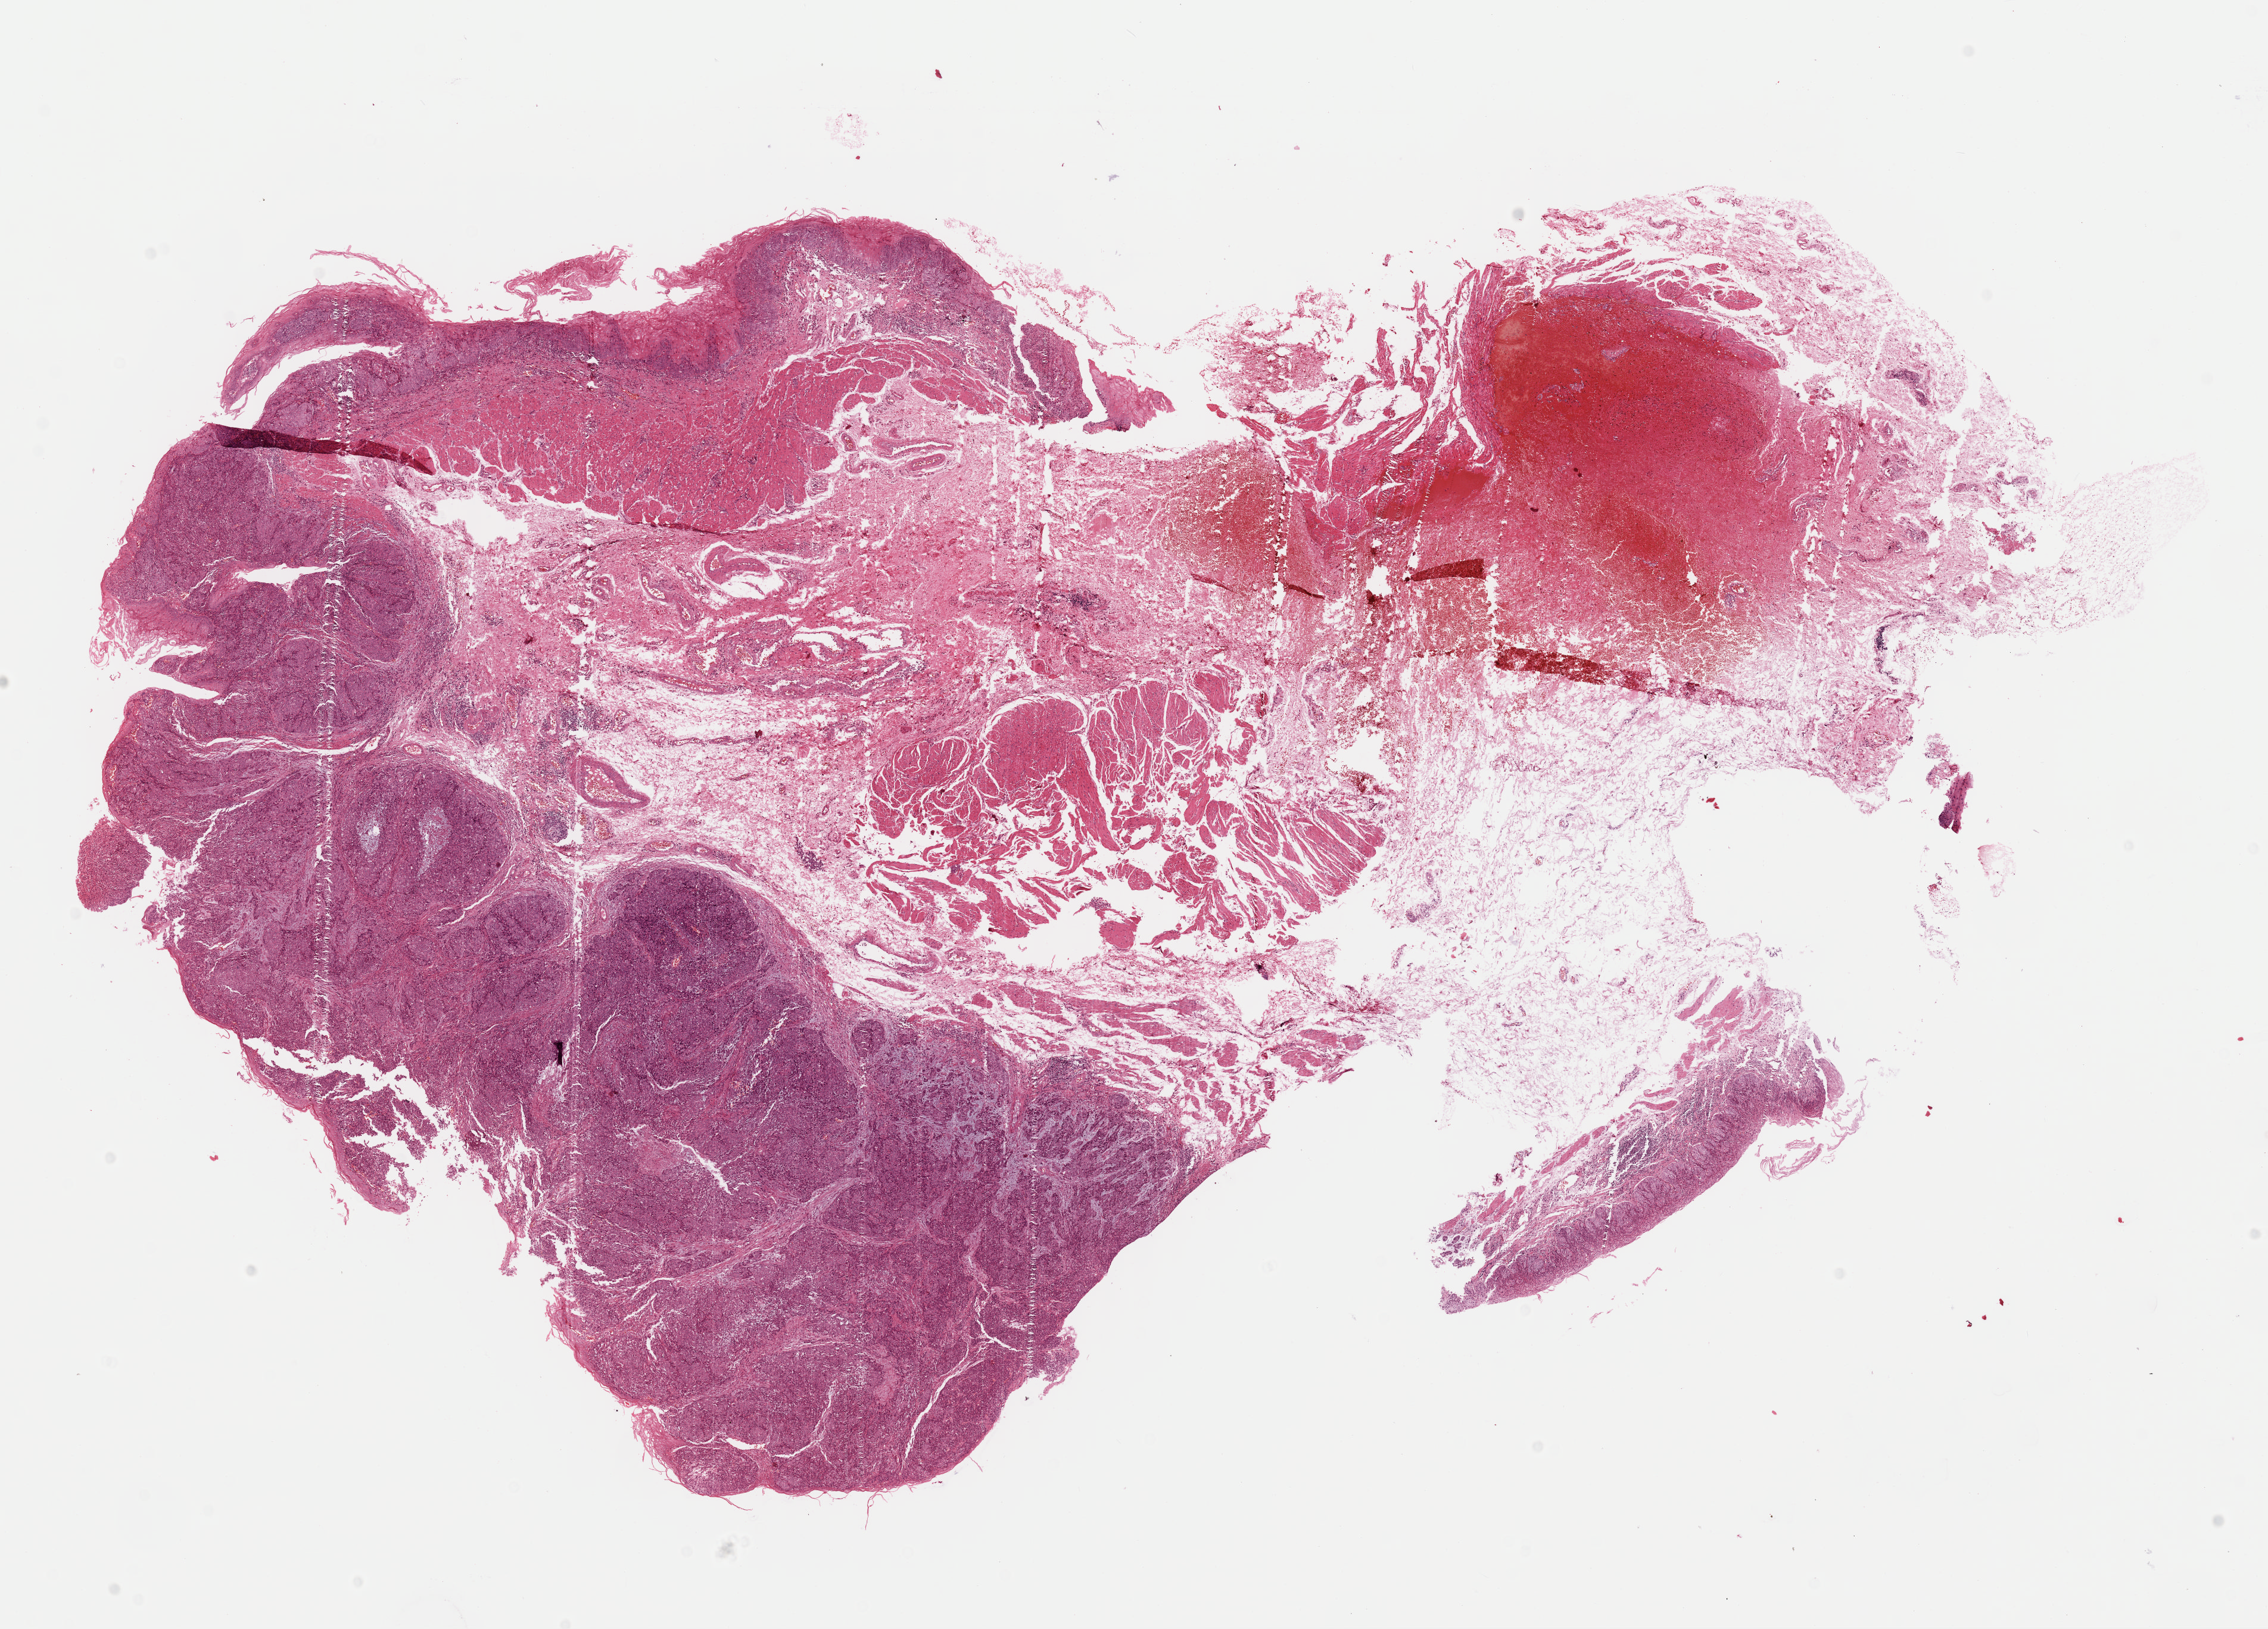
Whole-slide histology image, Hematoxylin and eosin (H&E) stained, low-resolution overview of the scanned area, about 15.0 x 10.8 mm (from a 40x scan). Formalin-fixed paraffin-embedded (FFPE) diagnostic section. Primary tumour sample from the esophagus. Male, age 77 years at initial diagnosis. Histologic grade: G2 (moderately differentiated).
AJCC pathologic stage: IIA (6th edition). Histologic diagnosis: Squamous cell carcinoma, NOS. TNM: T3 N0 M0.